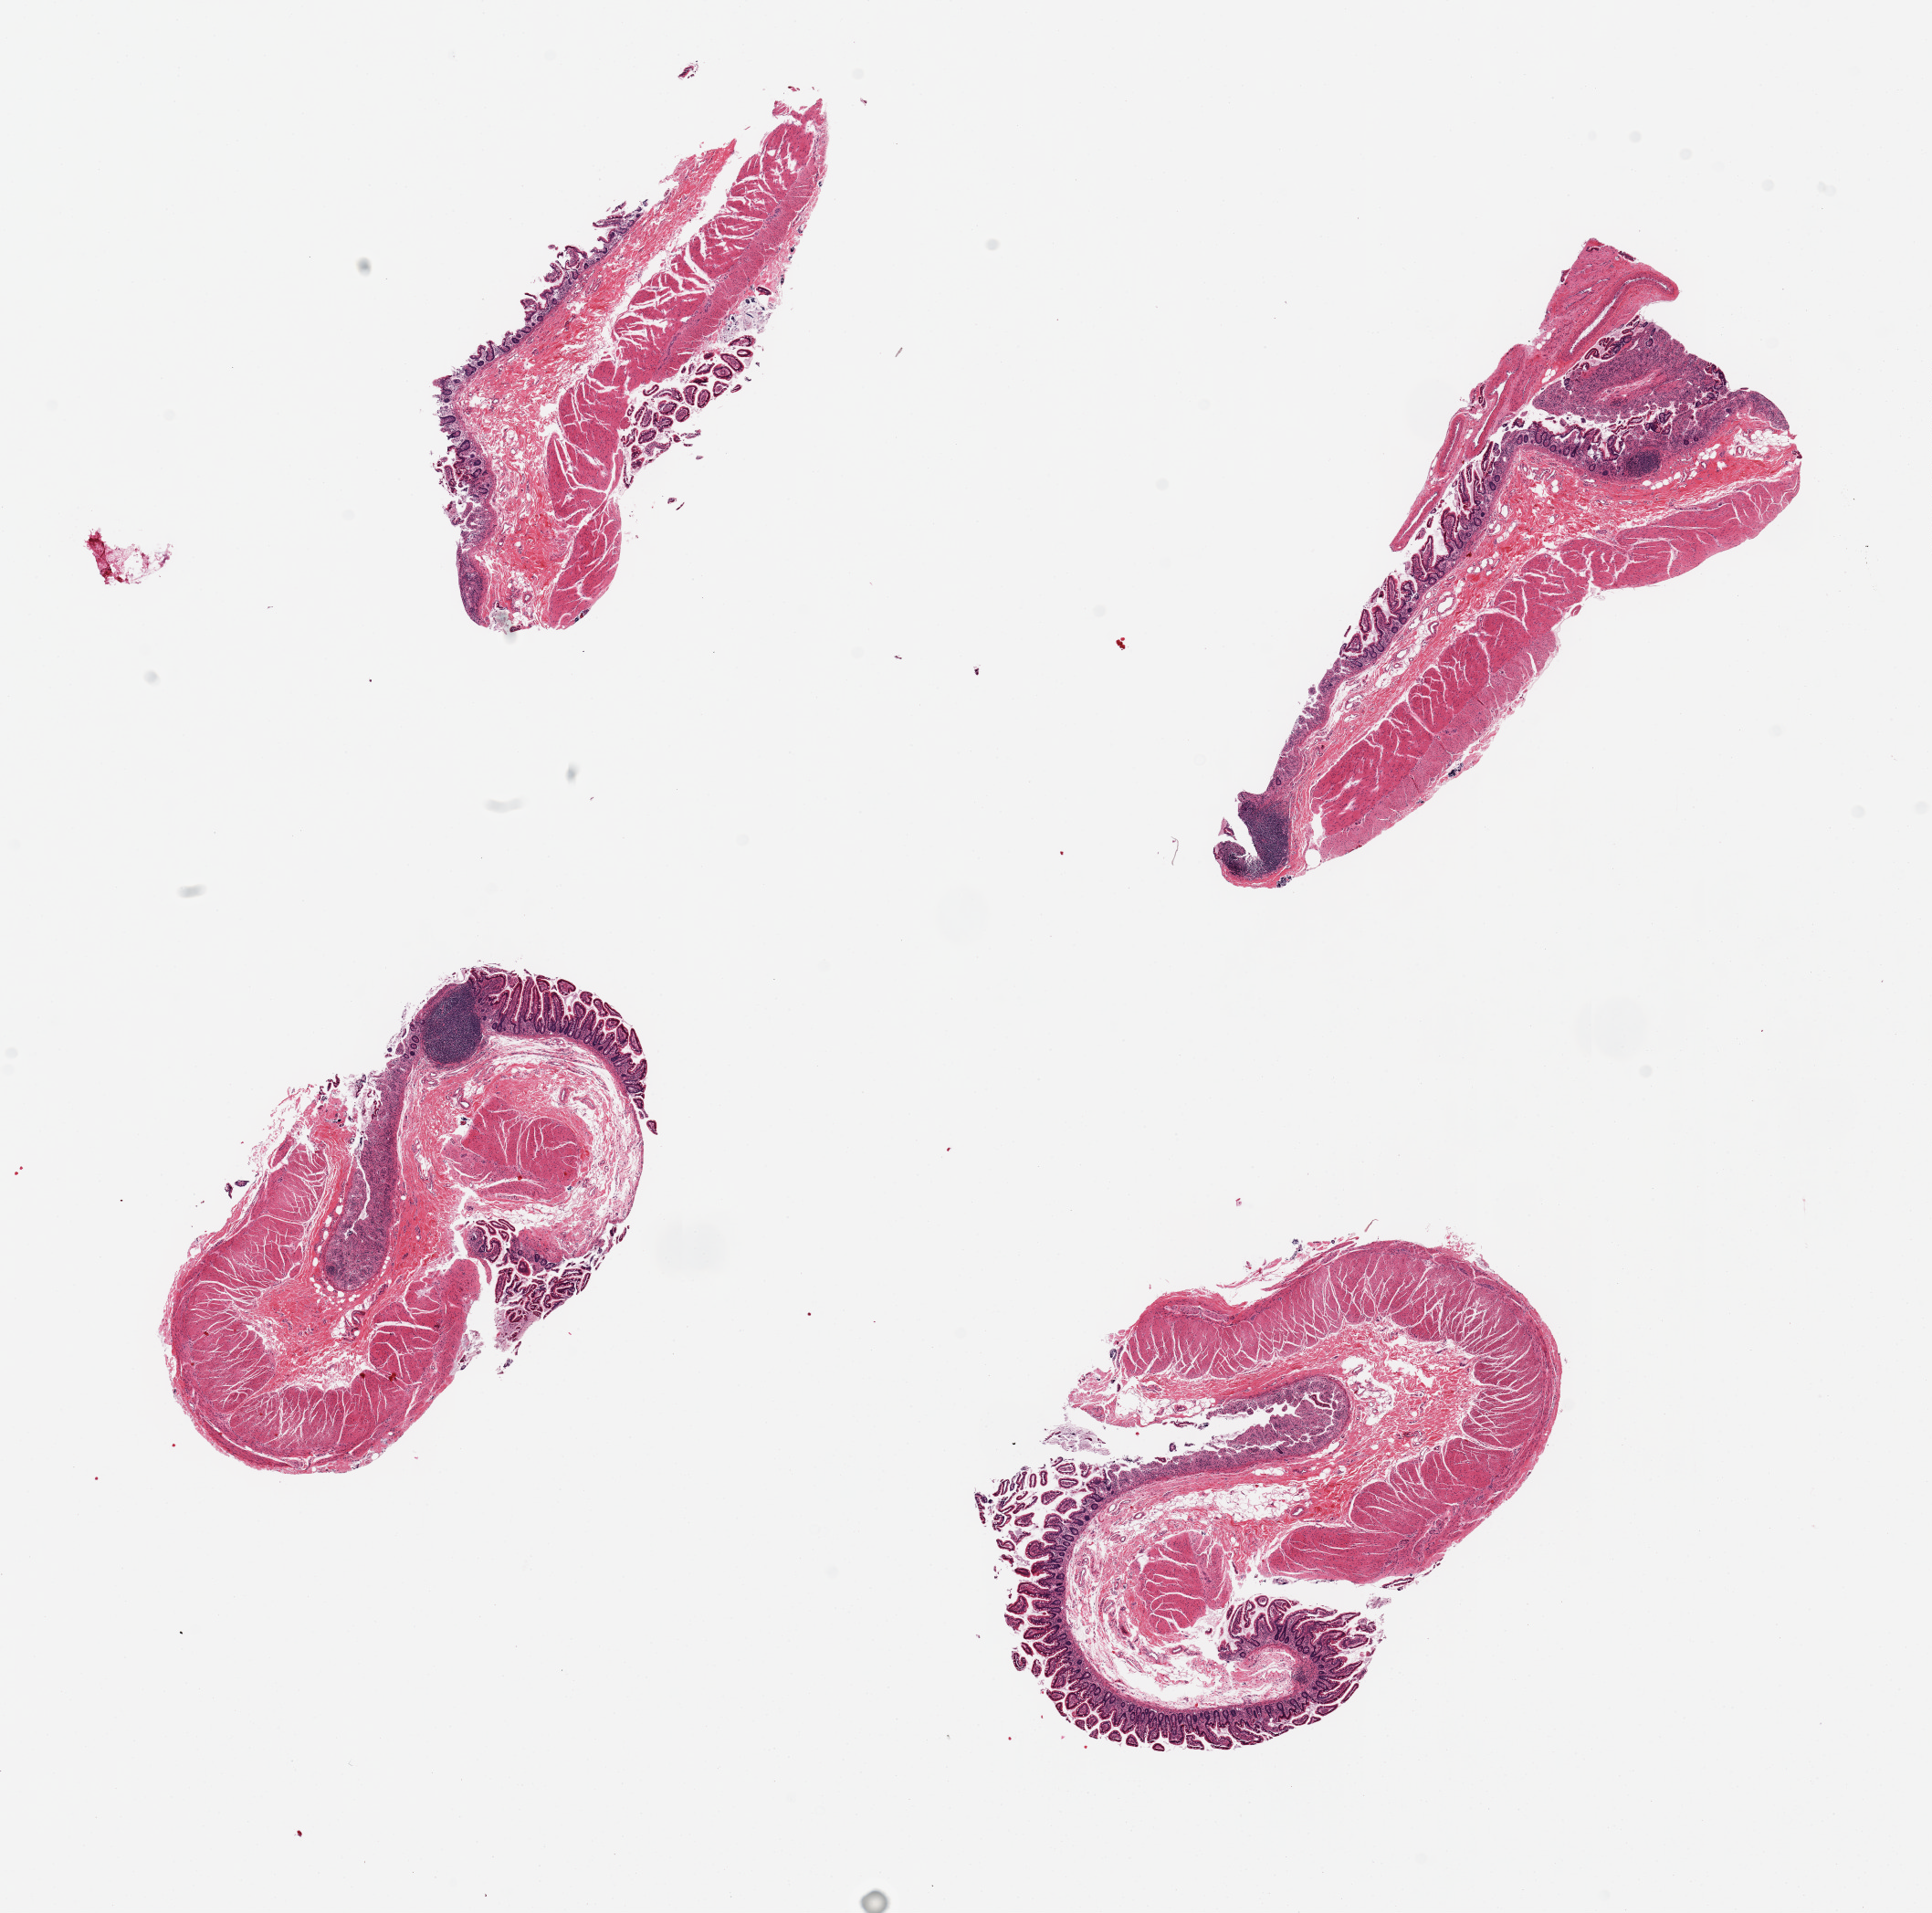
Whole-slide image, hematoxylin and eosin (H&E) stain, a low-resolution overview of the entire scanned area, about 16.7 x 16.6 mm (from a 20x scan); PAXgene-fixed, paraffin-embedded tissue; sampled site (target tissue): ileum; tissue donor sample. Donor: female.
Reviewer comment on this tissue sample: 4 pieces; full thickness sections (muscularis not target) with few lymphoid follicles.